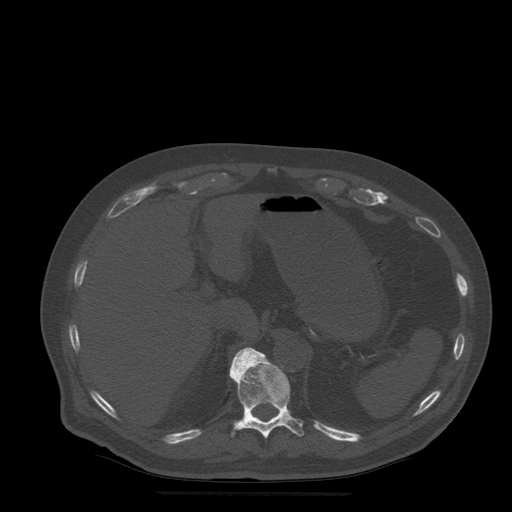
CT including the spine, one axial slice; position 244 of 522 along the scan axis; bone window (W 1800 / L 400 HU); 1.25 mm slice thickness; 512 × 512 image matrix, field of view 420 × 420 mm. Patient age 72 years. From the clinical record (not read from this slice): primary cancer: prostate.
Structures marked on this image (semi-automatic segmentation, software-assisted and operator-edited):
- T11 vertebra: box from (x=230, y=348) to (x=305, y=439) px
- T12 vertebra: (x=236, y=352)–(x=240, y=355)